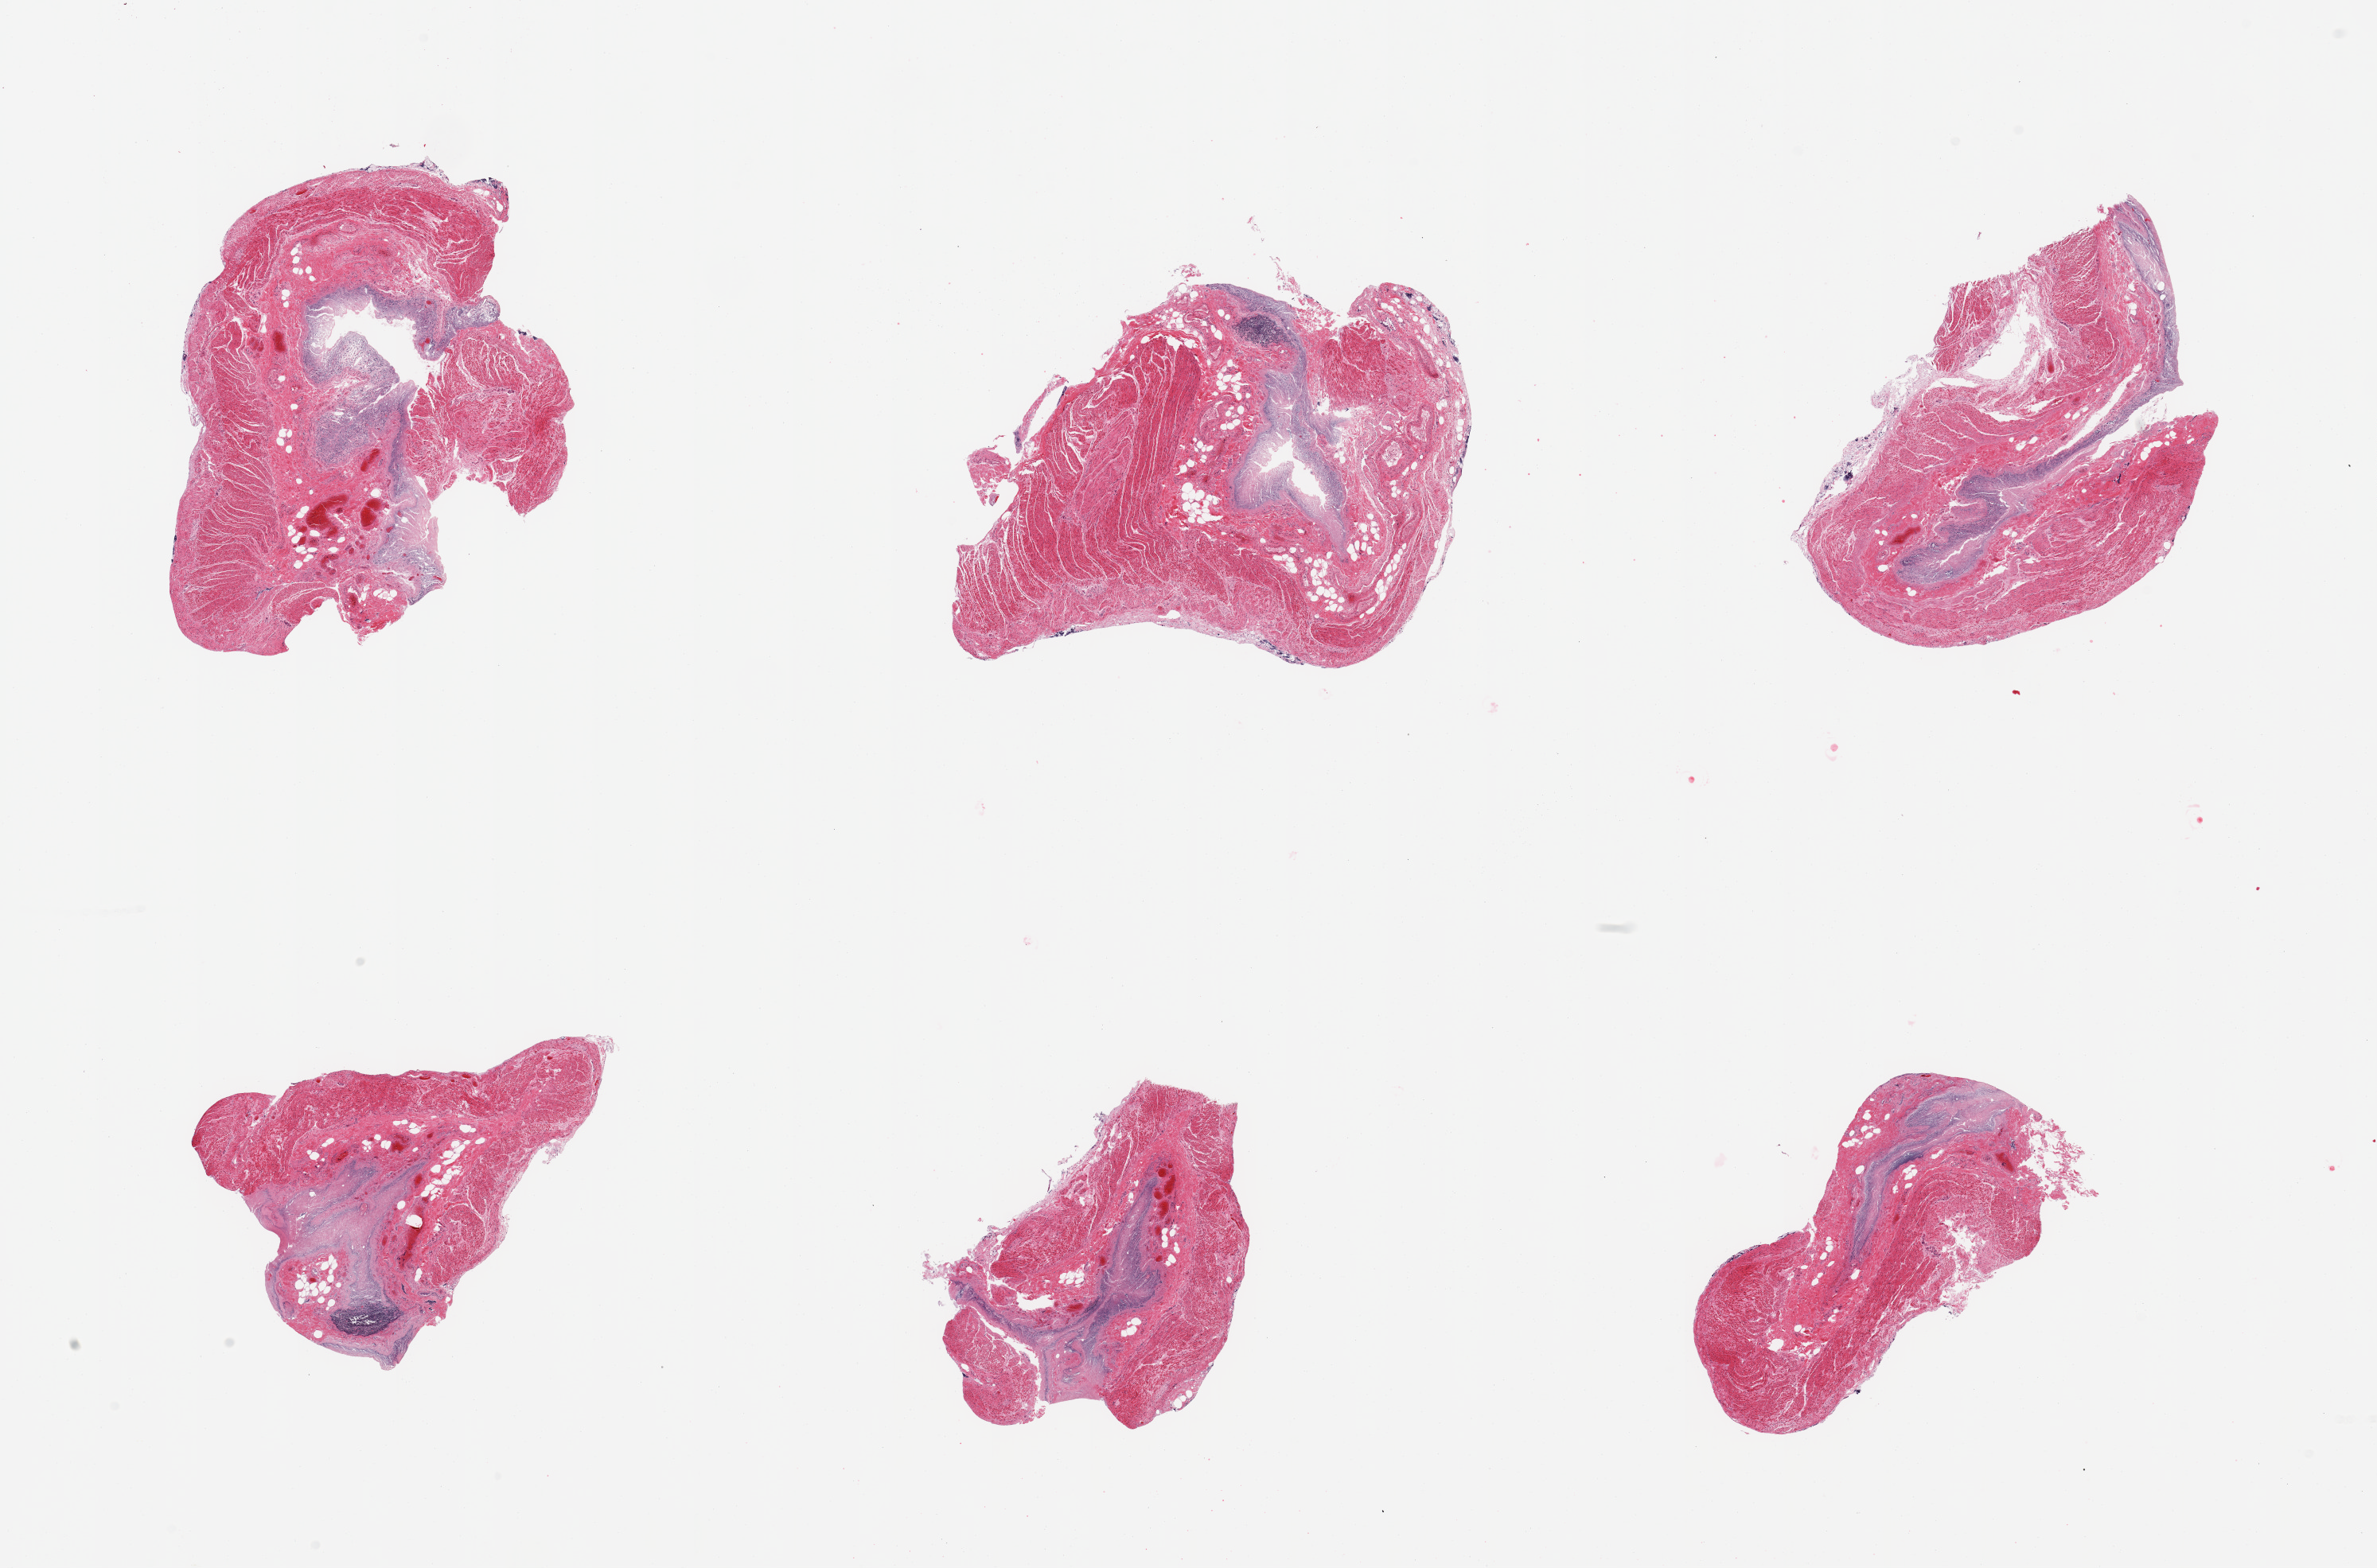
Whole-slide image, haematoxylin and eosin stain — whole scanned area (about 23.6 x 15.6 mm, acquisition: 20x scan) shown as a low-resolution overview. PAXgene-fixed paraffin-embedded (PFPE) section. Sampled site (target tissue): transverse colon. Donor tissue sample. Donor sex: male.
Review note (as recorded): 6 pieces; mucosa is entirely autolyzed, muscularis better preserved.